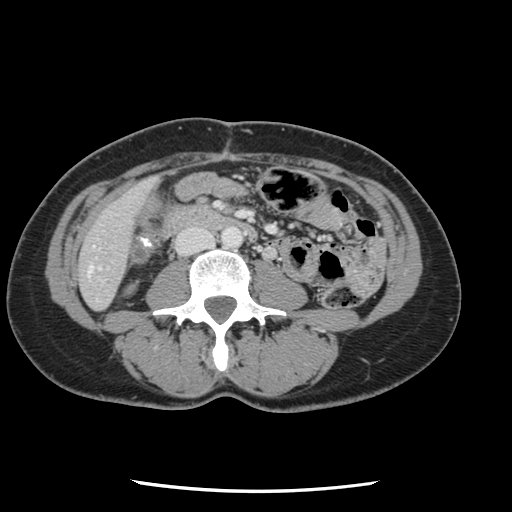
Contrast-enhanced abdominal CT, one axial slice; position 16 of 134 along the scan axis; 120 kVp; intravenous contrast given; soft-tissue window (W 400 / L 40 HU); 512 × 512 image matrix, field of view 330 × 330 mm. Female patient, age 43 years. From the clinical record (not read from this slice): diagnosis: colorectal cancer liver metastases, imaged before liver resection; multiple liver metastases: yes; largest metastasis: 3.4 cm.
Annotated regions visible in this slice (expert manual segmentation):
- hepatic veins: box from (x=89, y=266) to (x=92, y=273) px
- liver: (x=80, y=181)–(x=152, y=309)
- planned liver remnant (the part of the liver to remain after resection): (x=80, y=180)–(x=153, y=309)